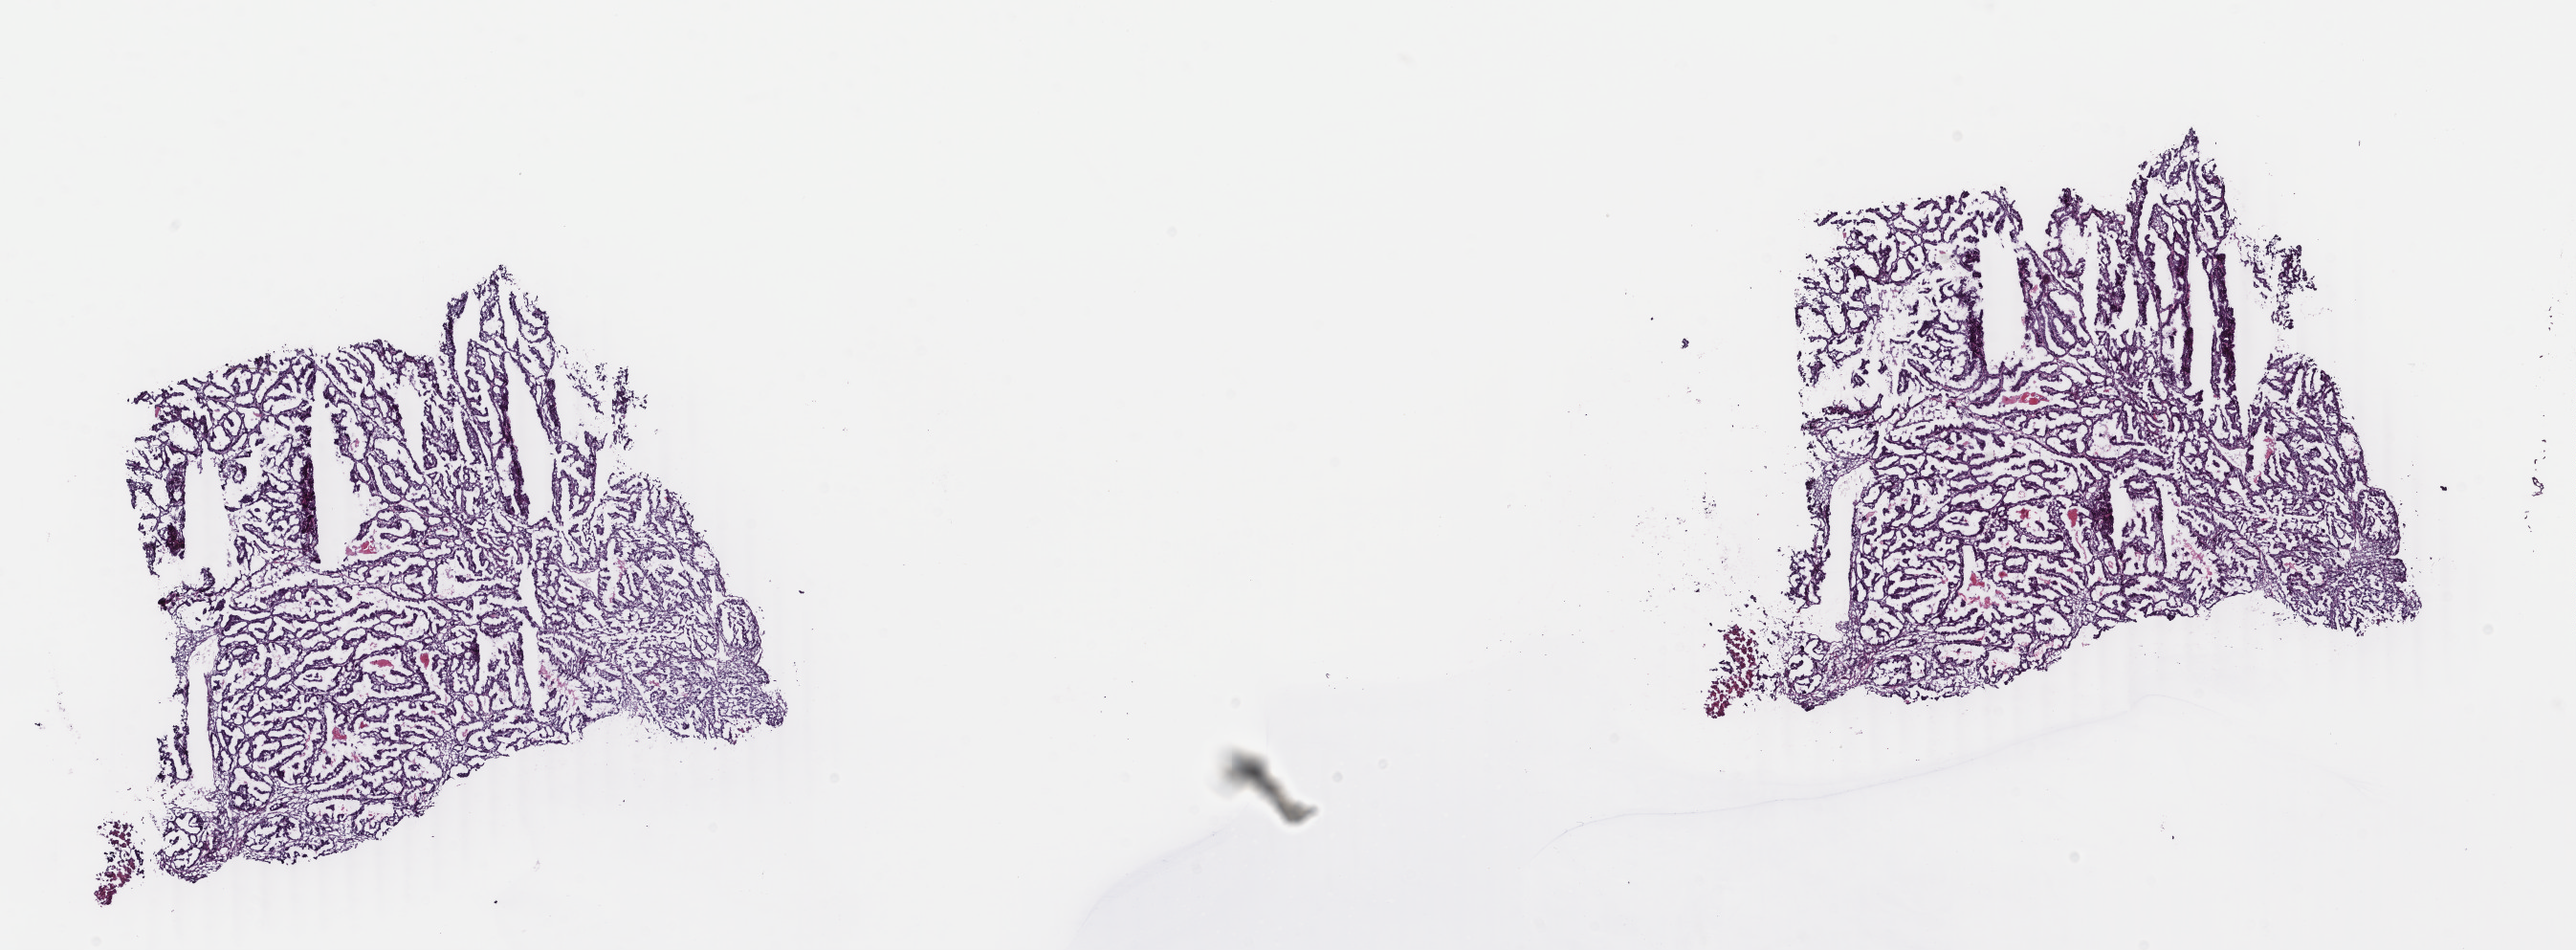
Whole-slide histology image, H&E, a low-resolution overview of the entire scanned area, about 21.4 x 7.9 mm; frozen section from the top of the tissue portion; sample: primary tumour, uterus. Female patient; age at initial diagnosis 71 years. Histologic grade: G1 (well differentiated). Slide review estimates, as recorded: tumour cells 95%, tumour nuclei 95%, normal cells 0%, stromal cells 4%, necrosis 1%. Infiltration values recorded for this section: lymphocyte infiltration 4%, monocyte infiltration 4%, neutrophil infiltration 0%.
Histologic diagnosis: Endometrioid adenocarcinoma, NOS (endometrium). FIGO stage: IA.